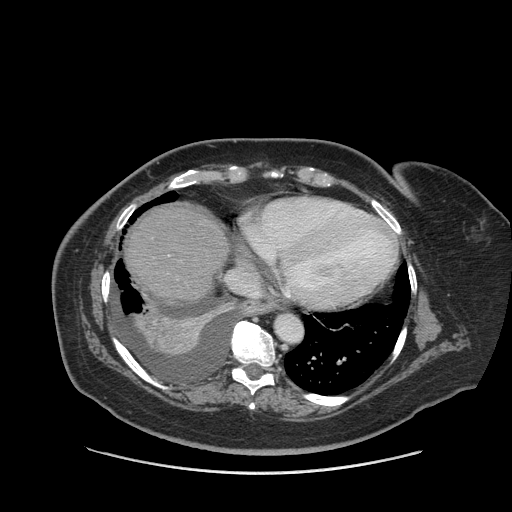
Contrast-enhanced abdominal CT (liver protocol), one axial slice; slice 78 of 91 in the series (ordered by position); reconstruction kernel STANDARD; soft-tissue window (W 400 / L 40 HU); 2.5 mm slice thickness; 512 × 512 image matrix, field of view 420 × 420 mm. From the clinical record (not read from this slice): diagnosis: hepatocellular carcinoma (patient treated with transarterial chemoembolisation; whether this scan precedes or follows treatment is not stated here); TNM stage (as recorded): Stage-I; Child-Pugh class: A; tumour differentiation: well differentiated; tumour nodularity: uninodular.
Structures marked on this image (semi-automatically segmented with operator editing):
- abdominal aorta: bounding box <275,315,303,343> (left, top, right, bottom; pixels)
- liver parenchyma outside the tumour (the mass and vessels are separate outlines, so this box may not span the whole liver): <124,204,228,300>